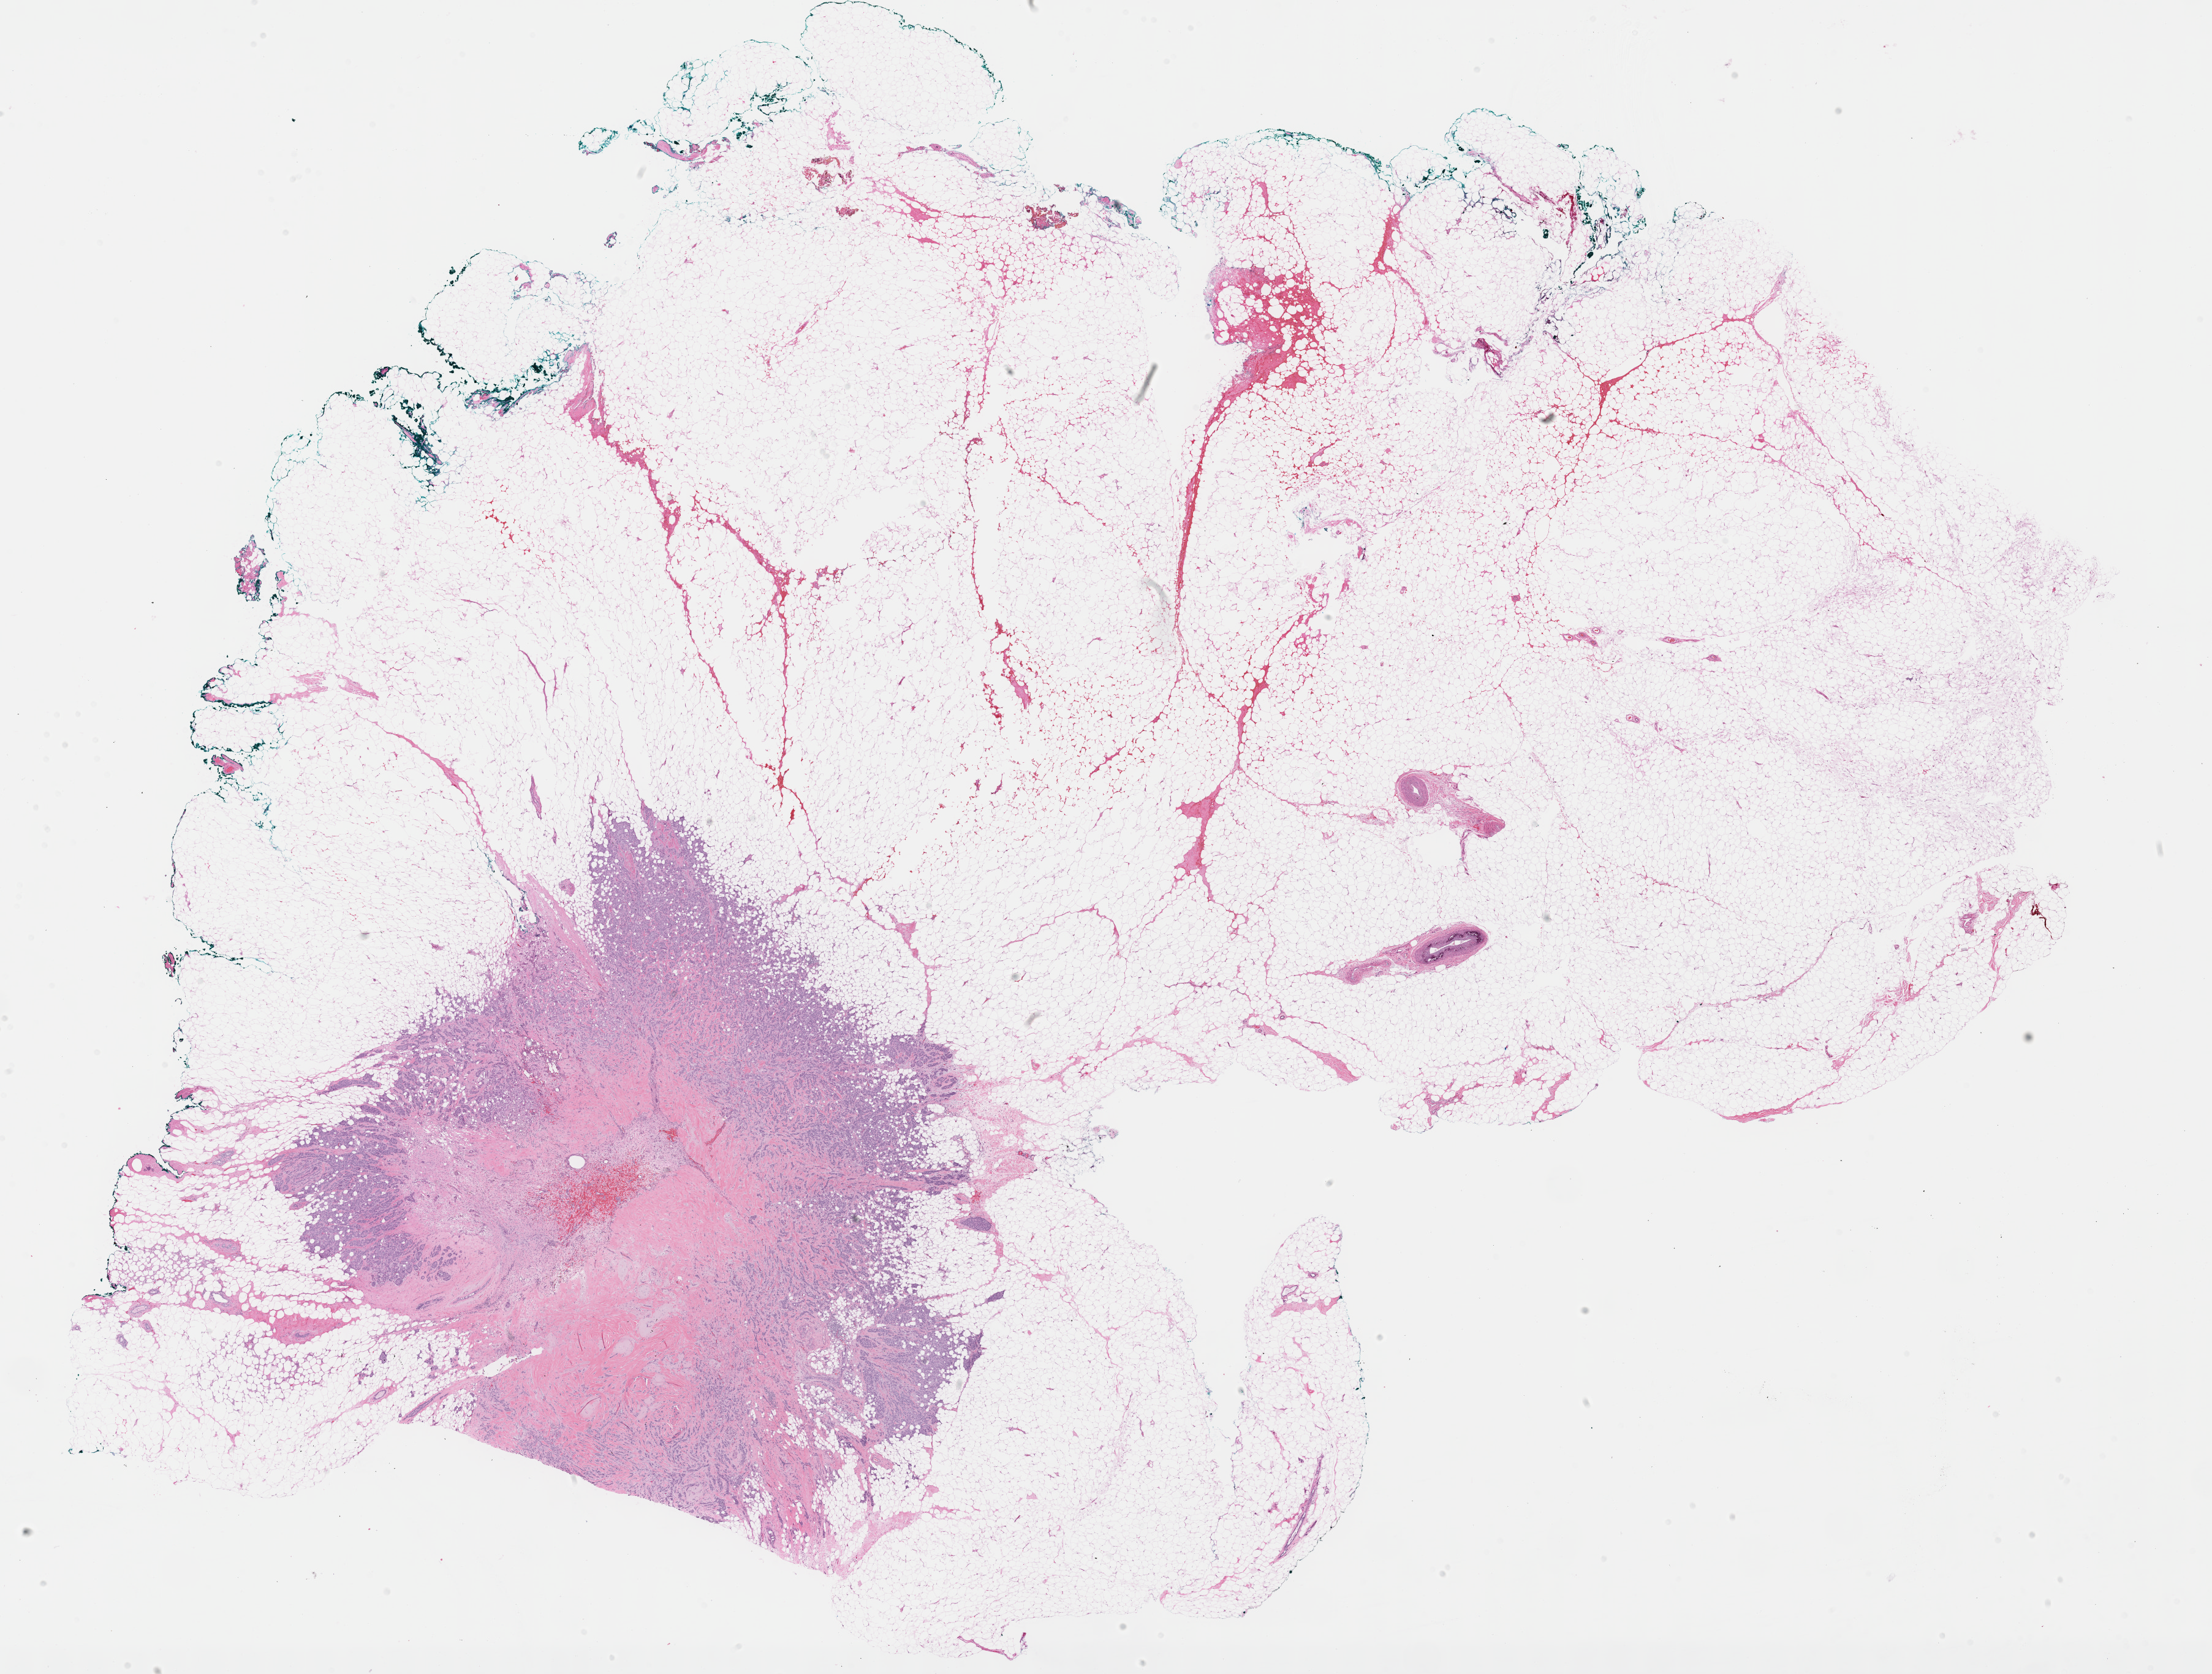
Digitized H&E tissue section (whole slide), low-resolution overview of the scanned area, about 29.2 x 22.1 mm (from a 40x scan). Formalin-fixed paraffin-embedded (FFPE) diagnostic section. Sample: primary tumour, breast. Female, age 77 years at initial diagnosis.
Histologic diagnosis: Lobular carcinoma, NOS.